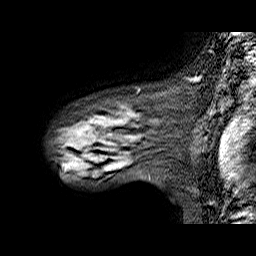
Breast MRI (dynamic contrast-enhanced), one sagittal slice; slice 48 of 60 in the series (ordered by position); dynamic contrast-enhanced series, time point 2 of 6 at this slice position (early post-contrast); 1.5 T; TE 6.3 ms, TR 32.9 ms; 4 mm slice thickness; 256 × 256 image matrix, field of view 200 × 200 mm. Female patient. From the clinical record (not read from this slice): setting: breast cancer imaged before/during neoadjuvant chemotherapy; receptor status: HER2-positive.
Structures marked on this image (semi-automatic segmentation, software-assisted and operator-edited):
- analysis volume of interest (the breast-tissue region the enhancement analysis was run in; not a lesion): bounding box <56,89,174,173> (left, top, right, bottom; pixels)
- tumour enhancement mask (voxels above the 100 % enhancement threshold inside the analysis volume of interest): <105,167,111,171>